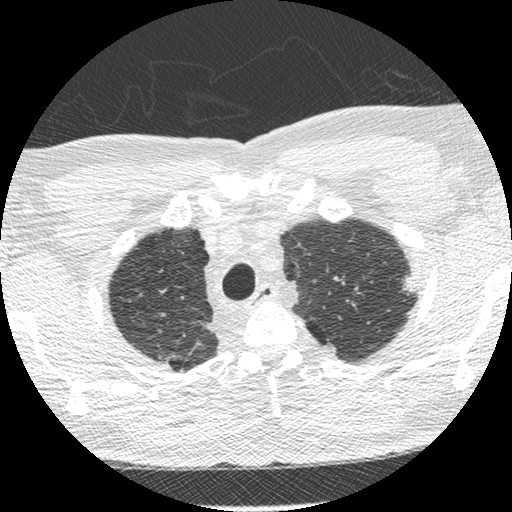
Low-dose screening chest CT, one axial slice. Position 241 of 275 along the scan axis. Reconstruction kernel STANDARD. Lung window (W 1500 / L -600 HU). 1.25 mm slice thickness. 512 × 512 image matrix, field of view 330 × 330 mm.
Structures marked on this image (expert manual segmentation):
- lesion 1 (tumor, upper lobe of left lung): bounding box (x1, y1, x2, y2) in pixels: (403, 275, 413, 295)